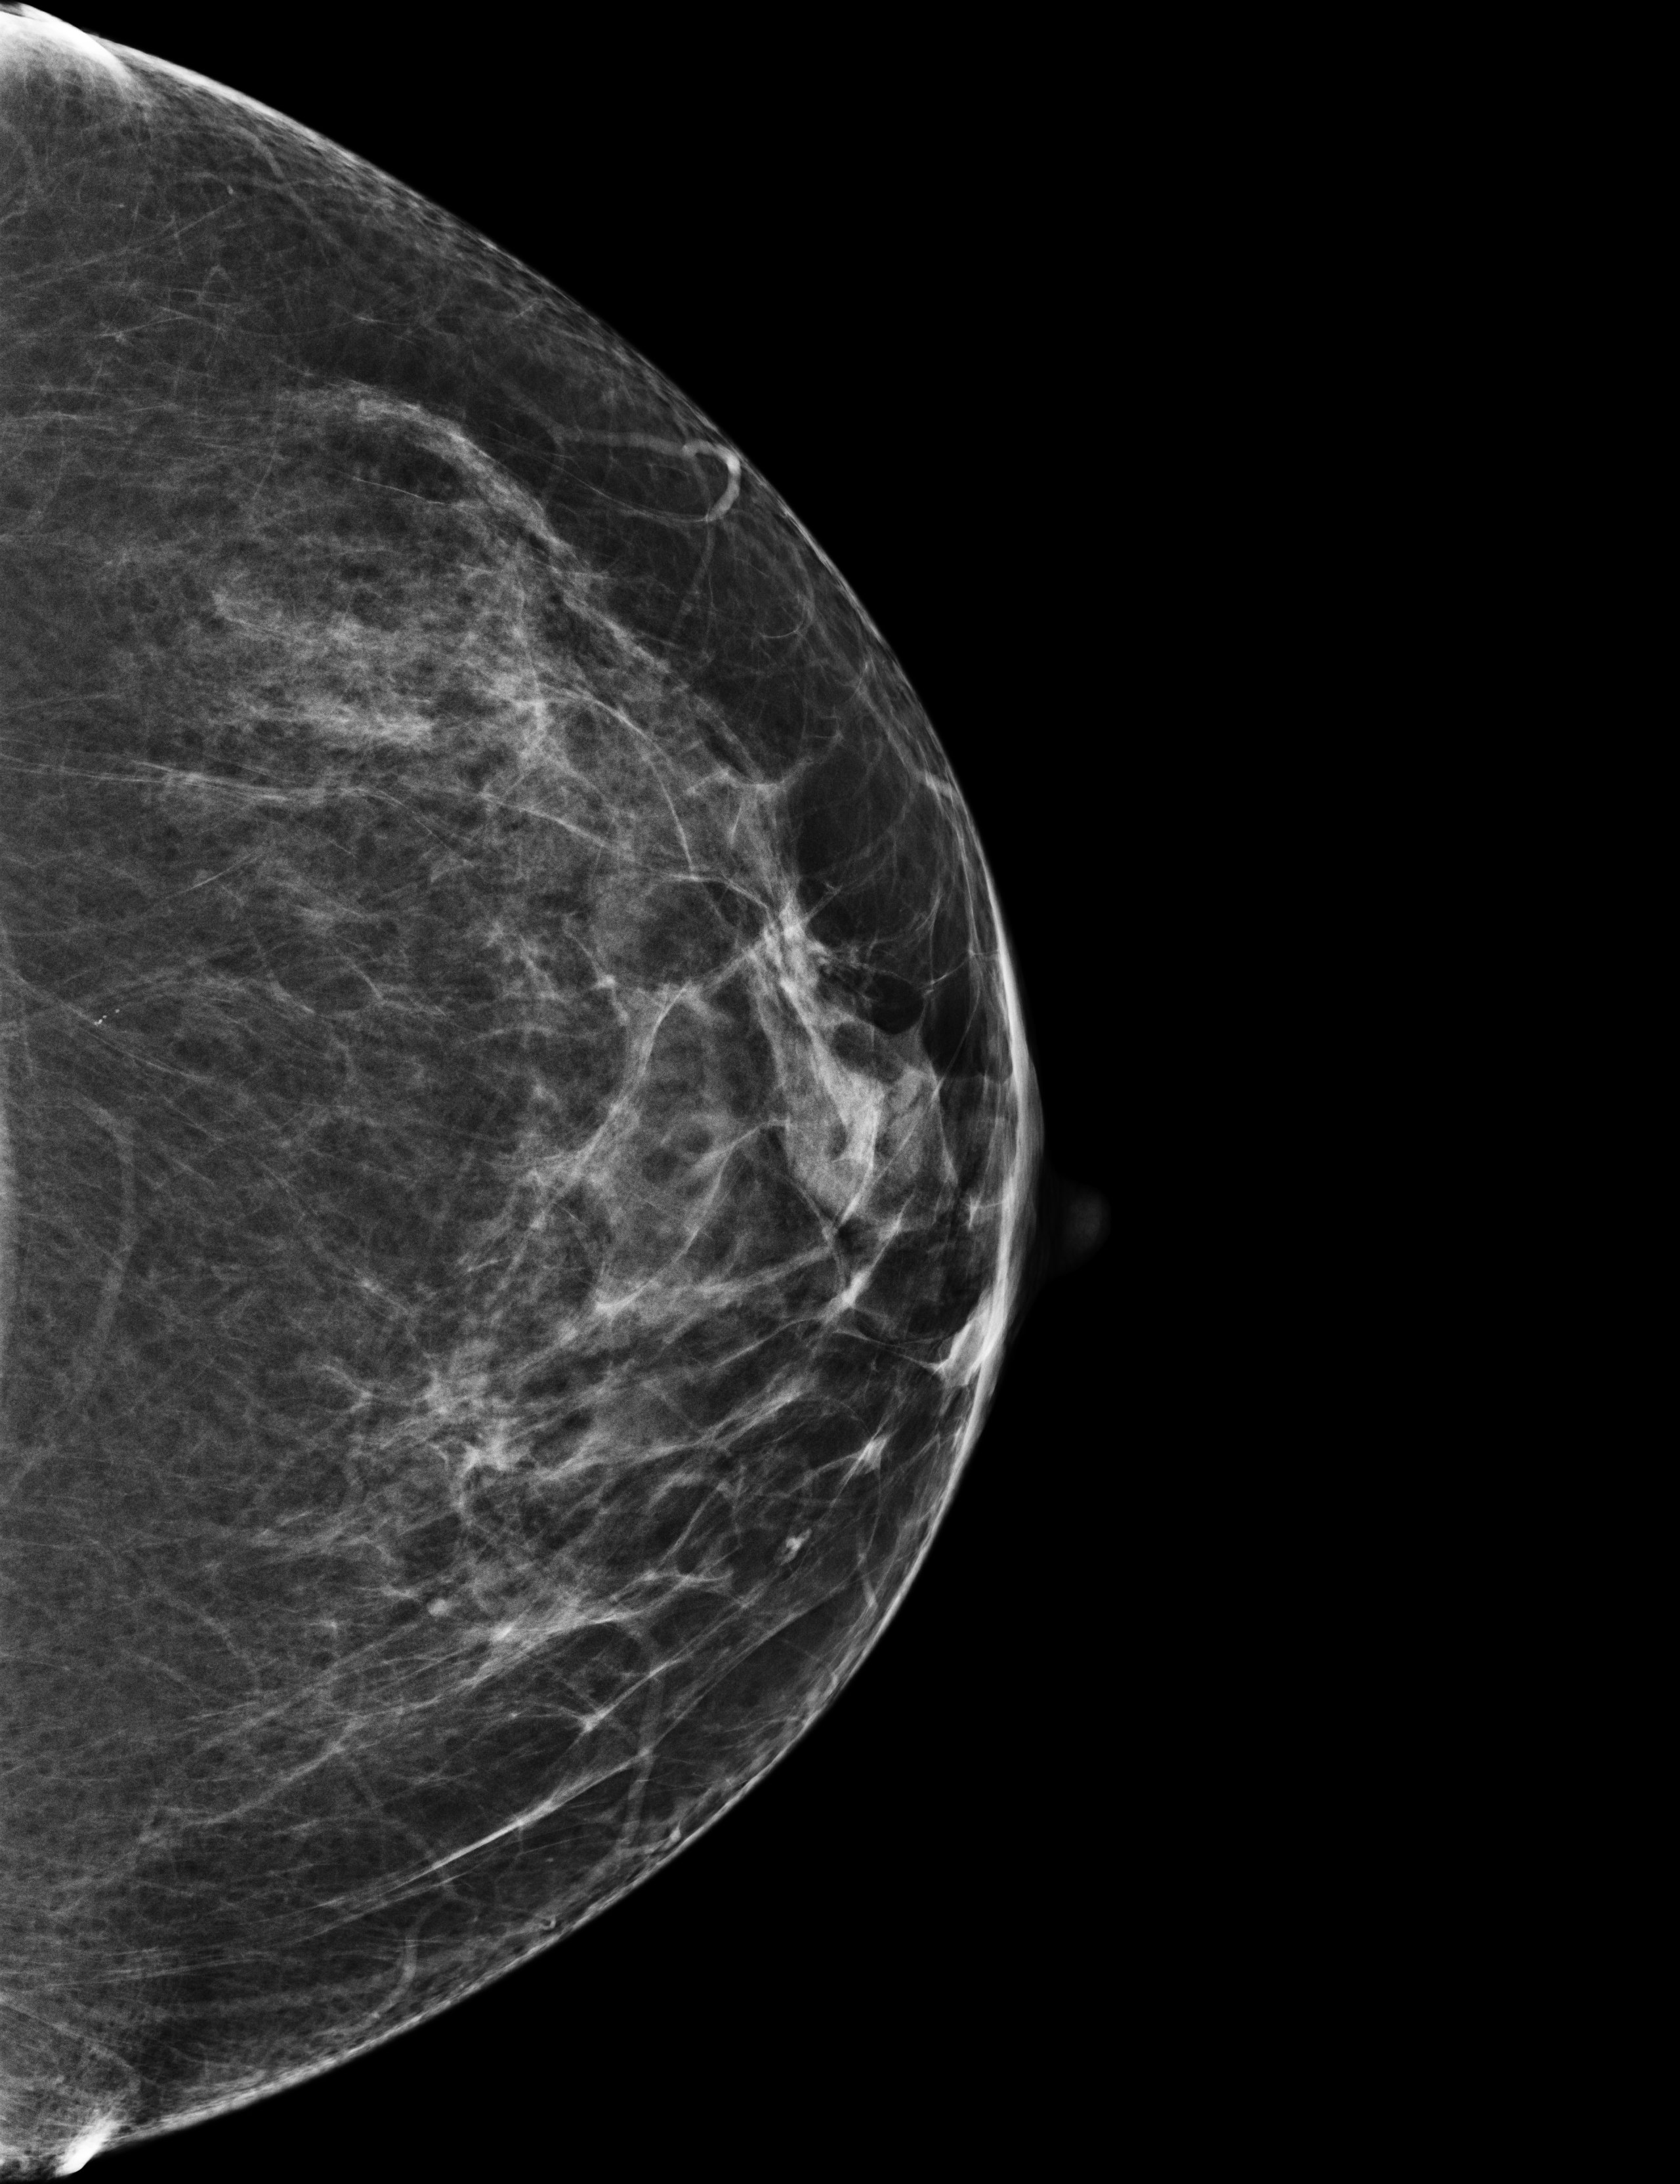
Screening examination; system: Selenia Dimensions. Female patient, age 57 years.
Image type: full-field digital mammogram. Breast: left. Projection: craniocaudal (CC) view.